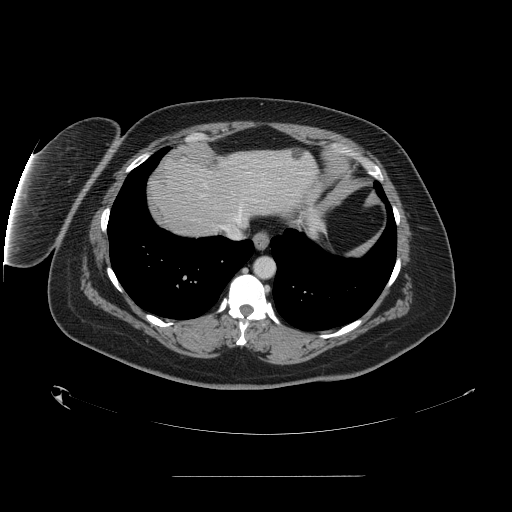
Contrast-enhanced abdominal CT, one axial slice; position 137 of 164 along the scan axis; 120 kVp; intravenous contrast given; soft-tissue window (W 400 / L 40 HU); 2.5 mm slice thickness; 512 × 512 image matrix, field of view 495 × 495 mm. Female patient, age 52 years. Case-level facts recorded for this patient, not image findings: diagnosis: colorectal cancer liver metastases, imaged before liver resection; multiple liver metastases: yes; largest metastasis: 3.5 cm.
Outlined on this slice (outlined manually by an expert reader):
- hepatic veins: bounding box (x1, y1, x2, y2) in pixels: (219, 202, 245, 239)
- liver: (149, 148, 317, 237)
- planned liver remnant (the part of the liver to remain after resection): (177, 148, 317, 225)
- liver metastasis: (291, 150, 304, 160)